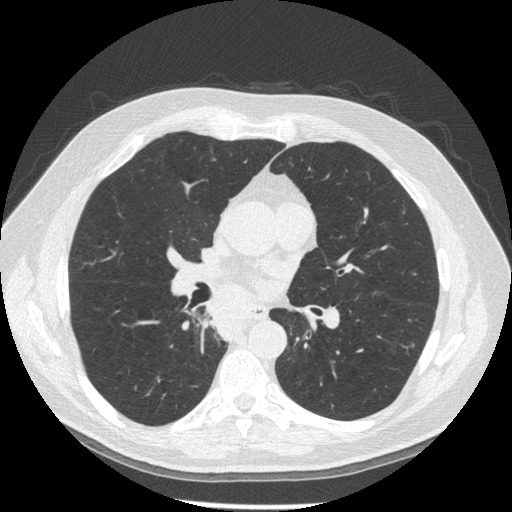
Low-dose screening chest CT, one axial slice; position 98 of 181 along the scan axis; reconstruction kernel STANDARD; 120 kVp; lung window (W 1500 / L -600 HU); 1.25 mm slice thickness; 512 × 512 image matrix, field of view 370 × 370 mm.
Structures marked on this image (outlined manually by an expert reader):
- lesion 1 (tumor, lower lobe of right lung): bounding box <201,302,247,342> (left, top, right, bottom; pixels)